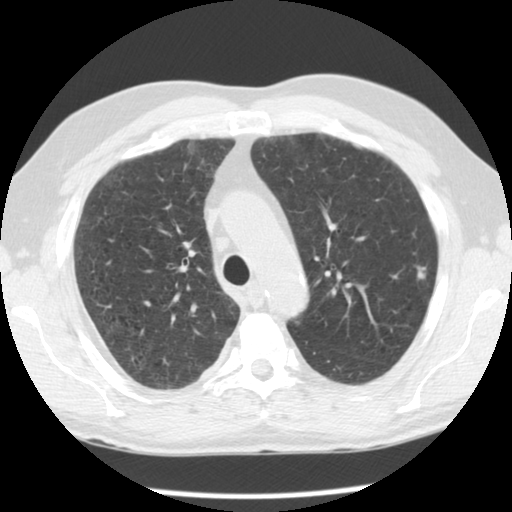
Low-dose screening chest CT, one axial slice. Position 83 of 113 along the scan axis. Reconstruction kernel STANDARD. Lung window (W 1500 / L -600 HU). 2.5 mm slice thickness. 512 × 512 image matrix, field of view 330 × 330 mm.
Structures marked on this image (manually delineated by an expert):
- lesion 3 (tumor, upper lobe of left lung): box from (x=417, y=266) to (x=426, y=279) px